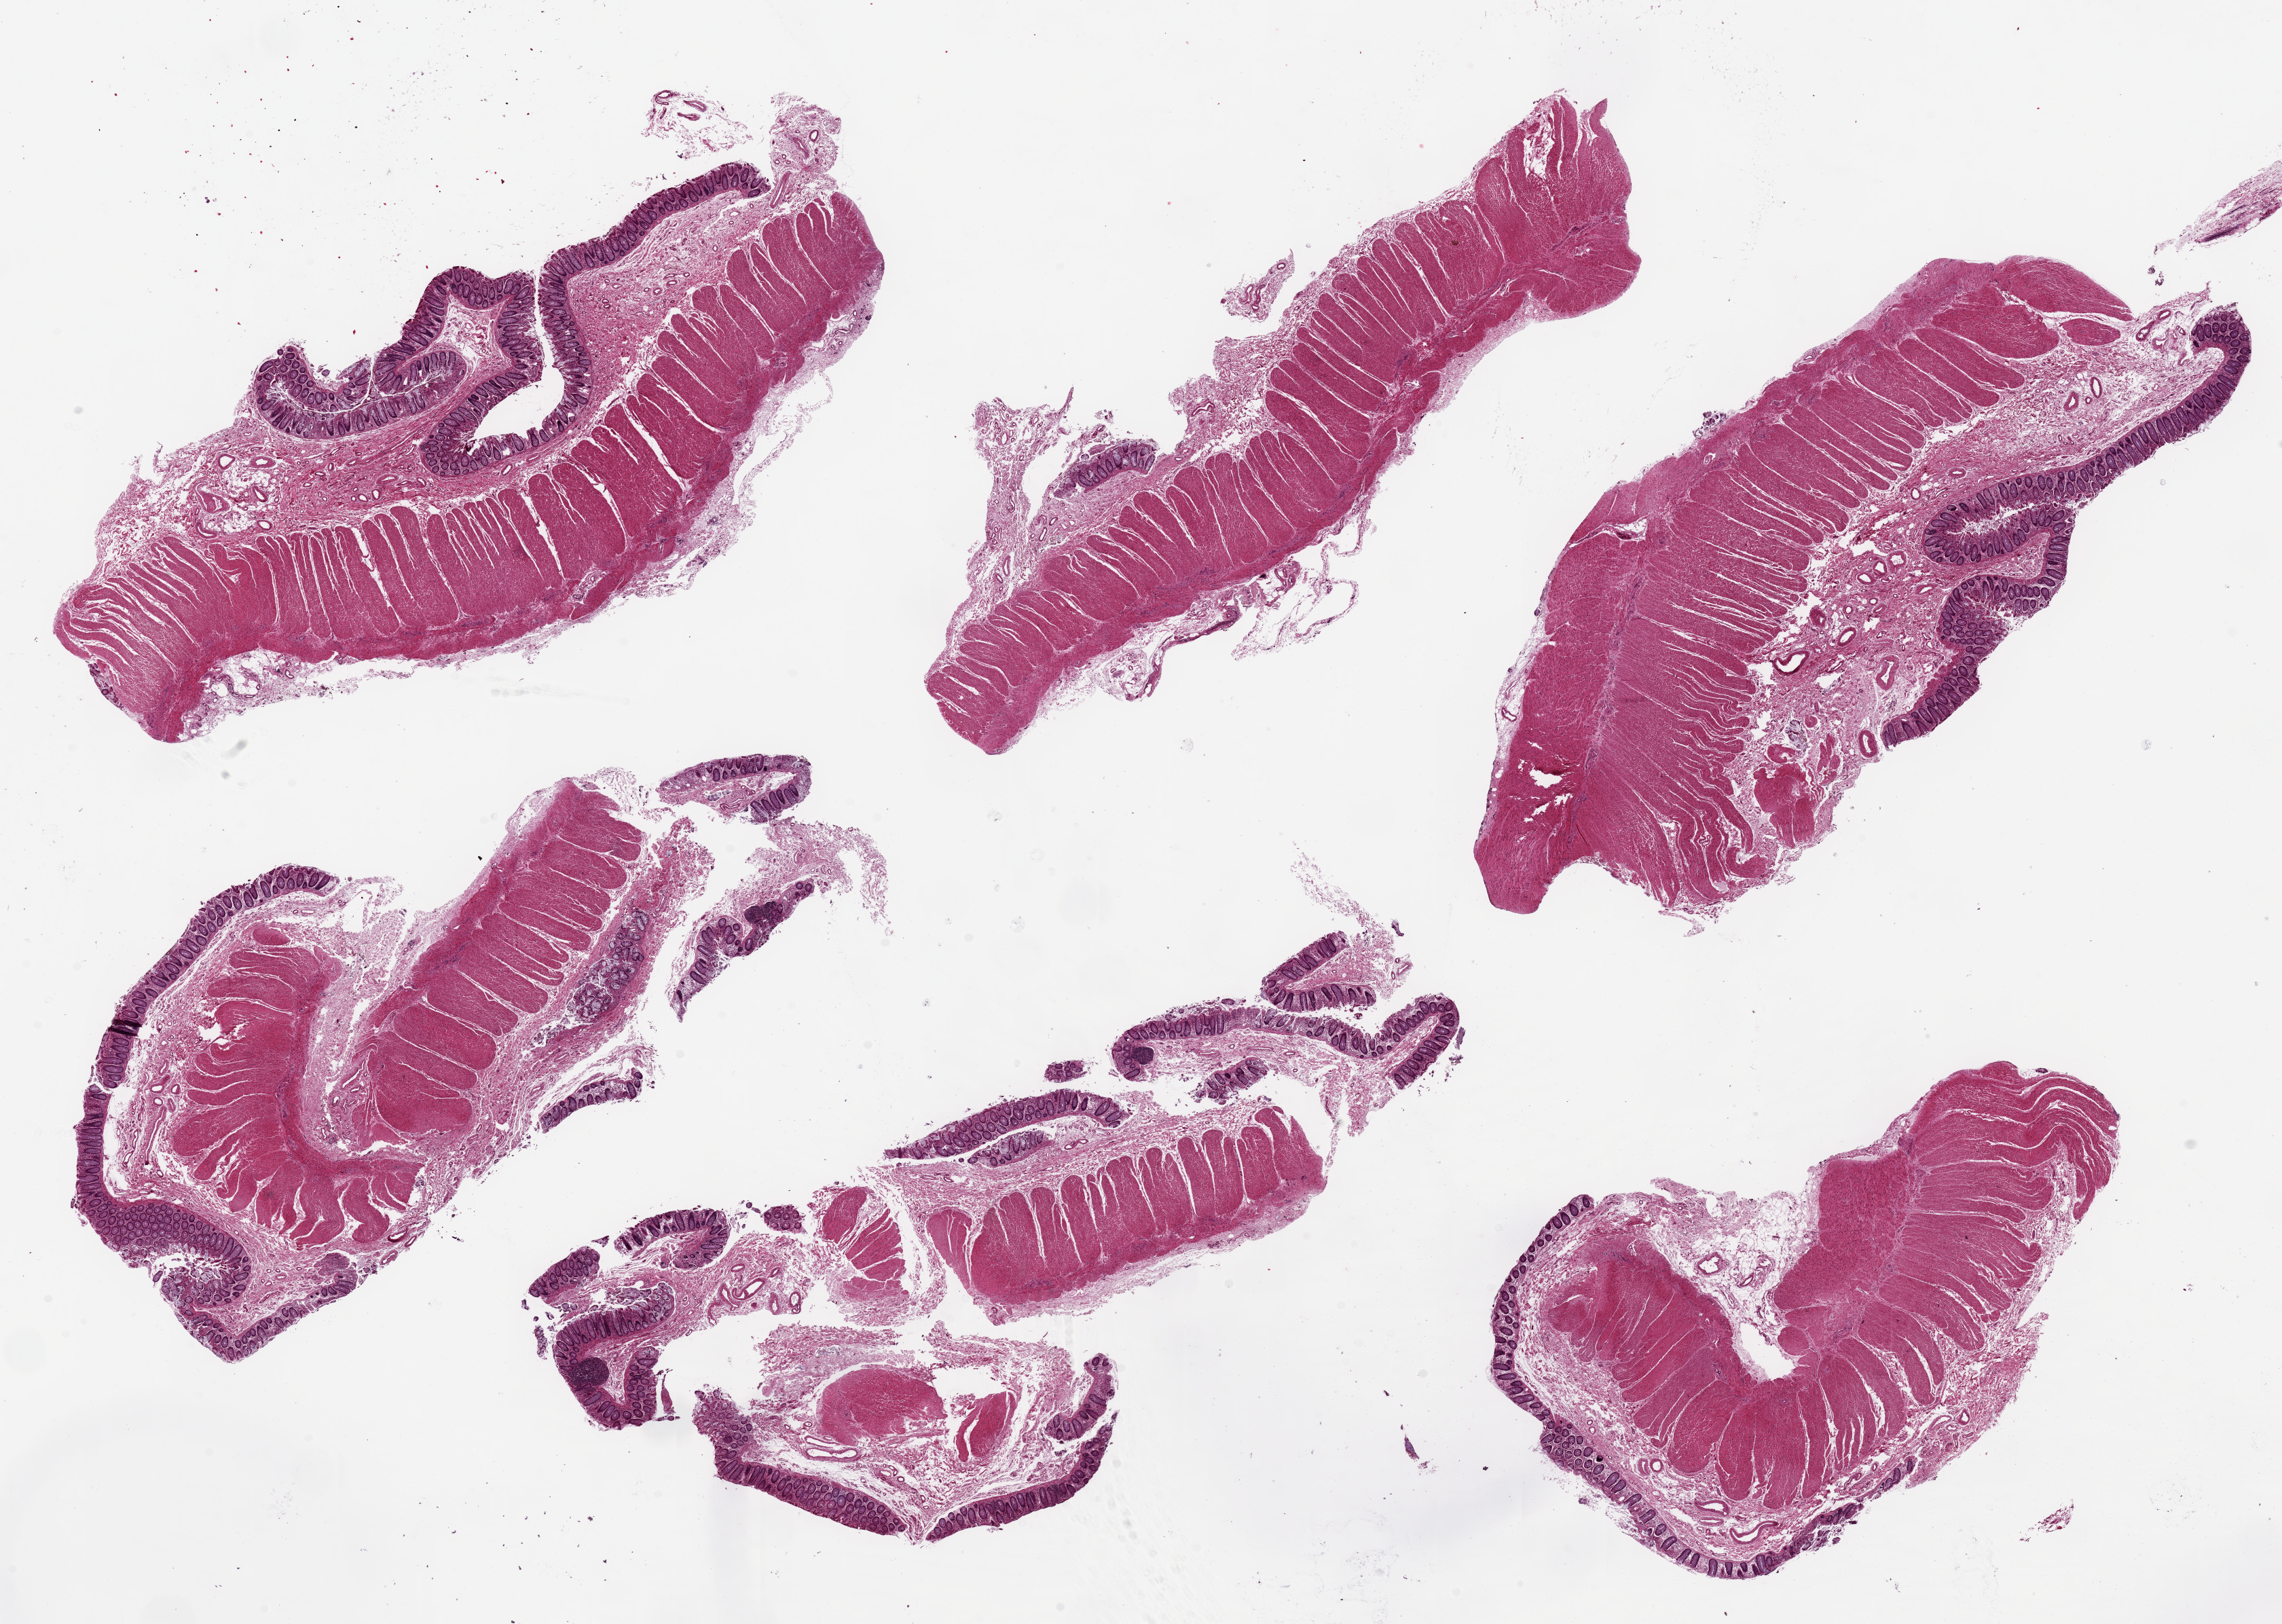
Whole-slide image, hematoxylin and eosin (H&E) stain, brightfield — shown as a low-resolution overview of the whole scanned area (about 26.6 x 18.9 mm), PAXgene-fixed, paraffin-embedded tissue, section of transverse colon (target tissue), donor tissue sample. Donor sex: female.
Review note (as recorded): 6 pieces up to ~11x4.7 mm.